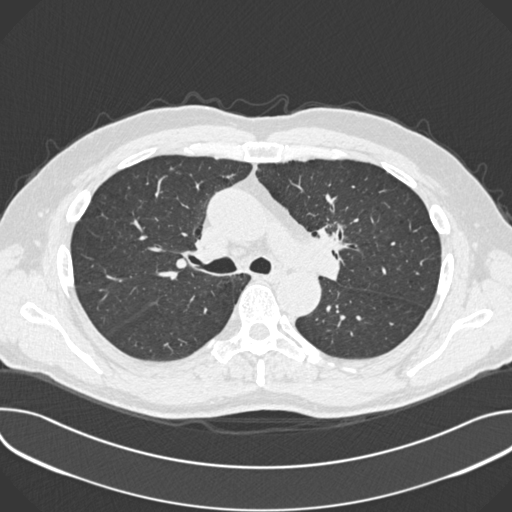
Low-dose screening chest CT, one axial slice. Position 243 of 361 along the scan axis. Reconstruction kernel B30f. Lung window (W 1500 / L -600 HU). 512 × 512 image matrix, field of view 380 × 380 mm.
Annotated regions visible in this slice (manually delineated by an expert):
- lesion 1 (tumor, upper lobe of left lung): bounding box <318,226,348,252> (left, top, right, bottom; pixels)